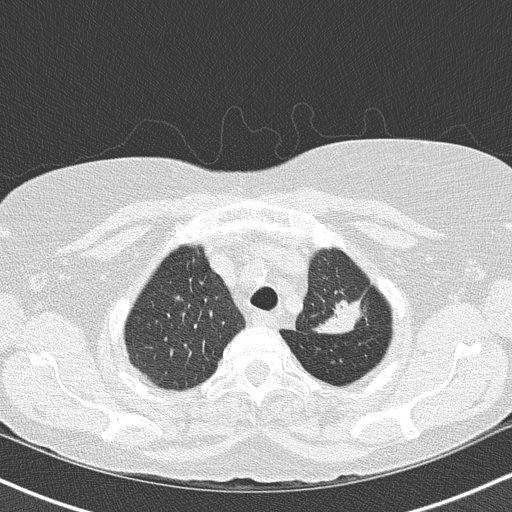
Axial slice from a low-dose chest CT screening exam. Third screening round (two years after baseline). Lung window (W 1500 / L -600 HU). 2 mm slice thickness. 120 kVp. Slice 126 of 147 in the series. 512 × 512 image matrix, field of view 320 × 320 mm. Female participant, aged 68 years at enrolment. Former smoker at enrolment.
Lesion marked by an expert reader, box from (x=288, y=237) to (x=379, y=343) px. Screening reader's record for this exam (one nodule recorded; not confirmed to be the boxed lesion): non-calcified nodule or mass ≥4 mm, left upper lobe, 5 × 5 mm, poorly defined margins, mixed attenuation, pre-existing on the prior screen: yes; interval growth: yes. Official screen result: positive, other. Lung cancer was diagnosed 42 days after this screen: adenocarcinoma, NOS, left upper lobe, poorly differentiated (G3), stage IB (AJCC 6th edition), 50 mm at pathology.